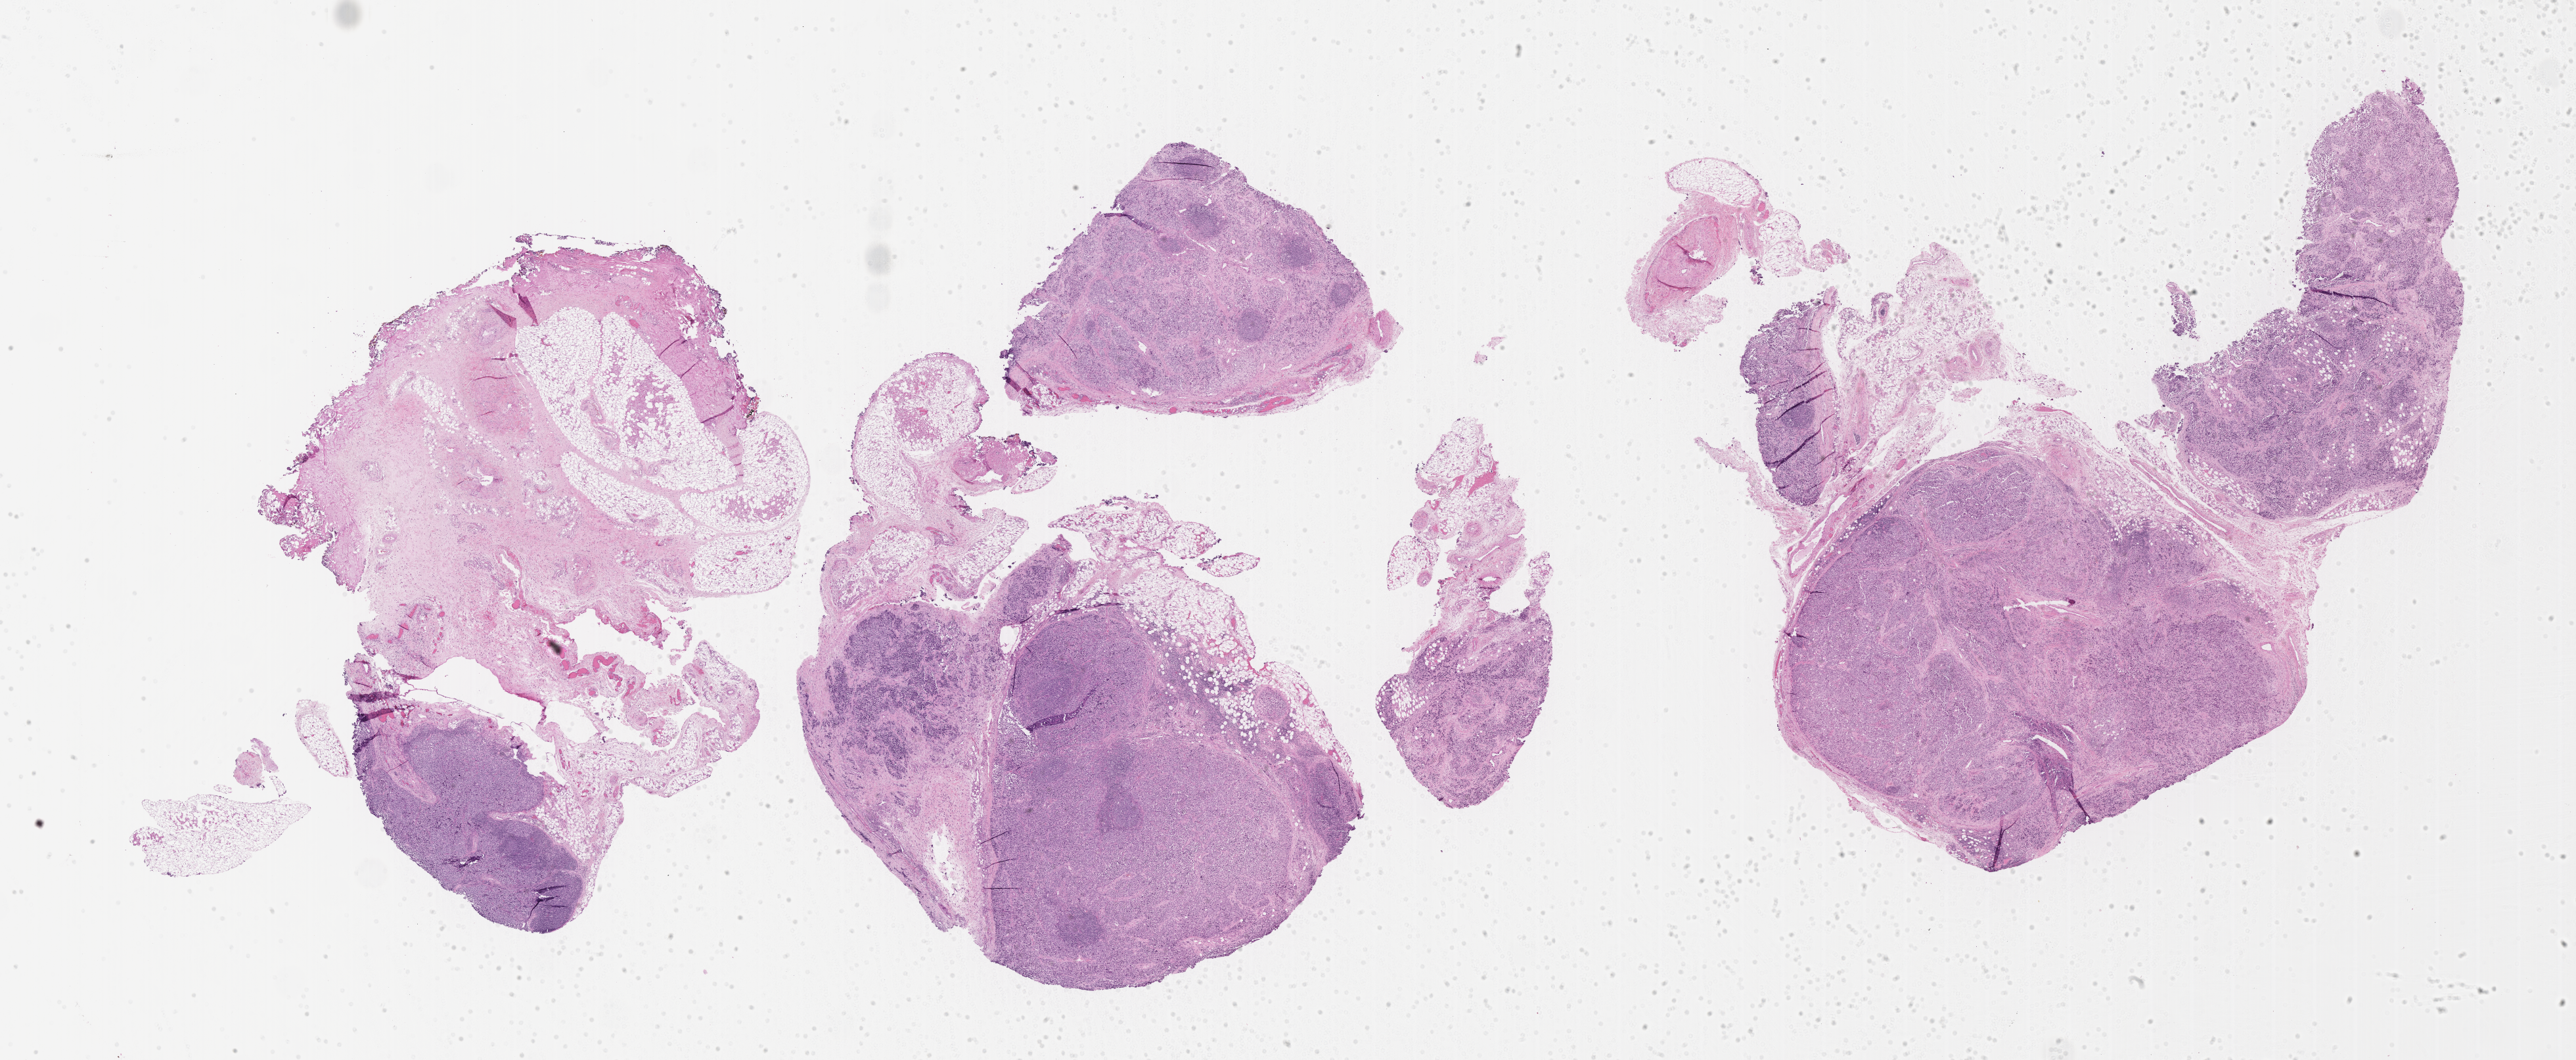
Whole-slide image, H&E stain of tumor tissue — shown as a low-resolution overview of the whole scanned area (about 31.7 x 13.0 mm). Formalin-fixed, paraffin-embedded (FFPE) tissue. Site: soft tissue, forearm. Patient: female, age 9.8 years at diagnosis.
Diagnosis: rhabdomyosarcoma; histological classification: alveolar rhabdomyosarcoma.